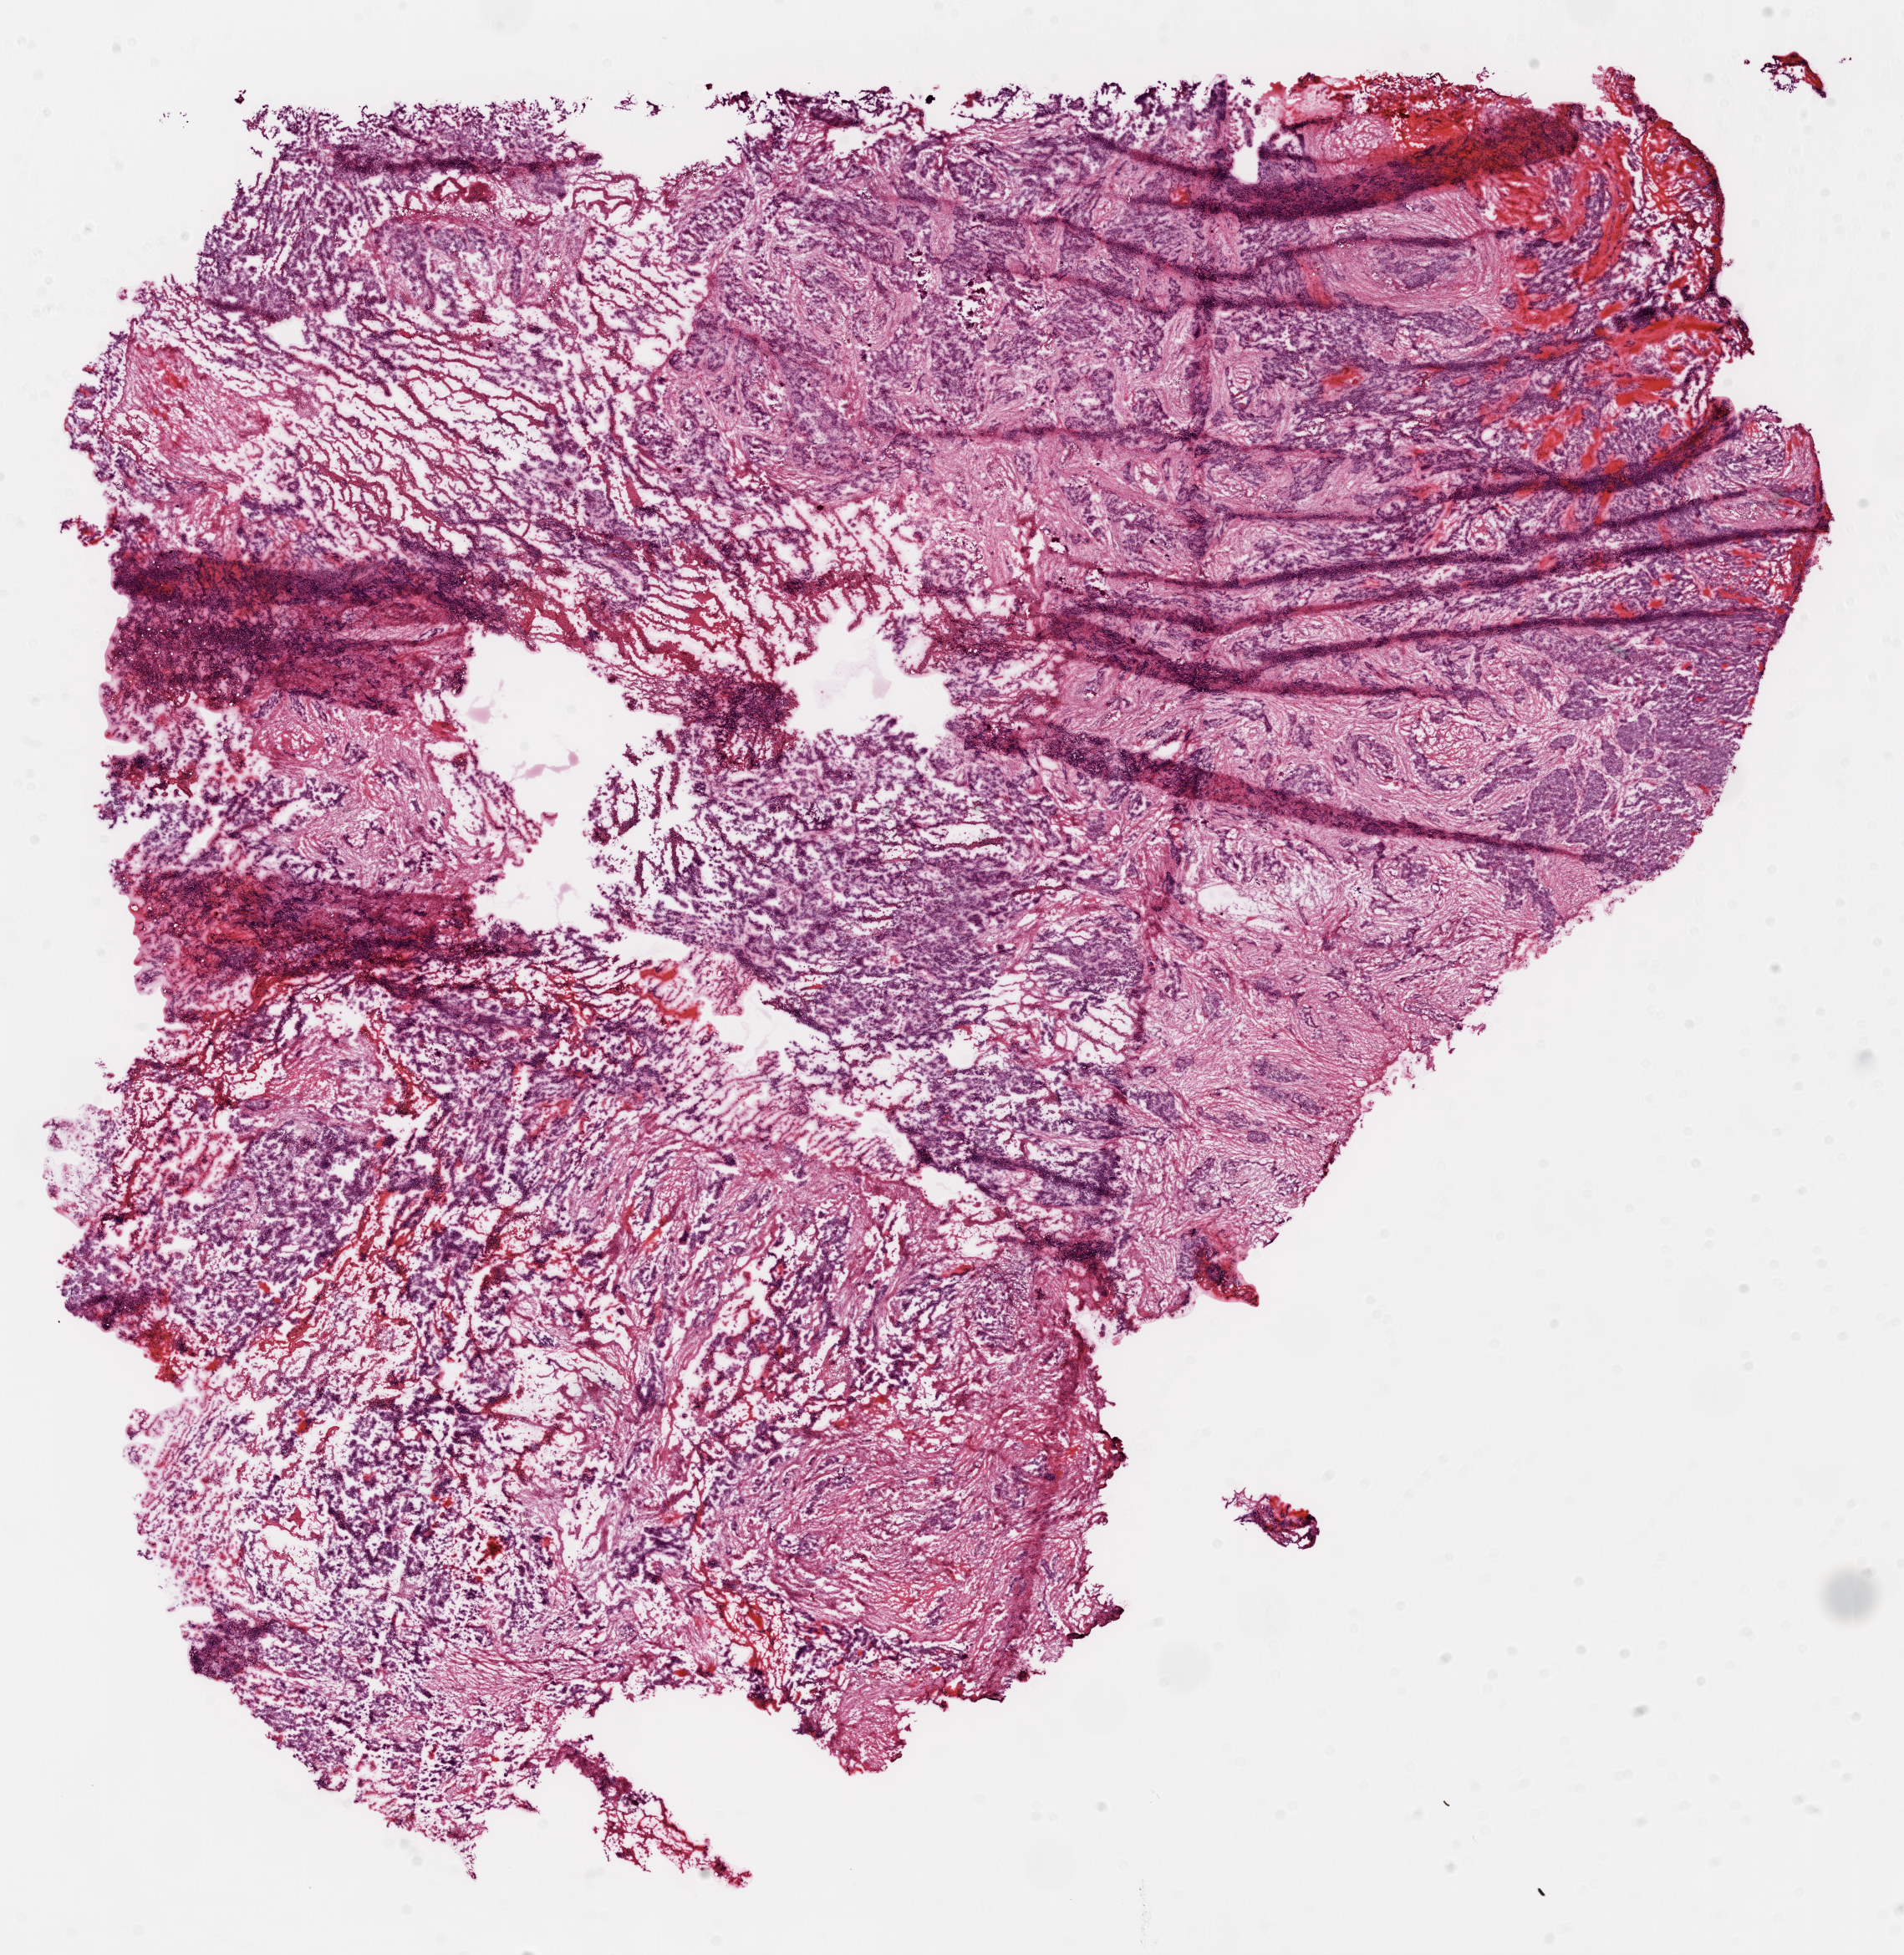
Whole-slide histology image, H&E-stained — shown as a low-resolution overview of the whole scanned area (about 18.4 x 18.9 mm). Frozen section from the top of the tissue portion. Primary tumour sample from the ovary. Female patient; age at initial diagnosis 65 years. Histologic grade: G3 (poorly differentiated). Pathologist review of this section (percent, as recorded): tumour cells 70%, tumour nuclei 85%, normal cells 0%, stromal cells 25%, necrosis 5%.
FIGO stage: IIIC. Pathologic diagnosis: Serous cystadenocarcinoma, NOS.